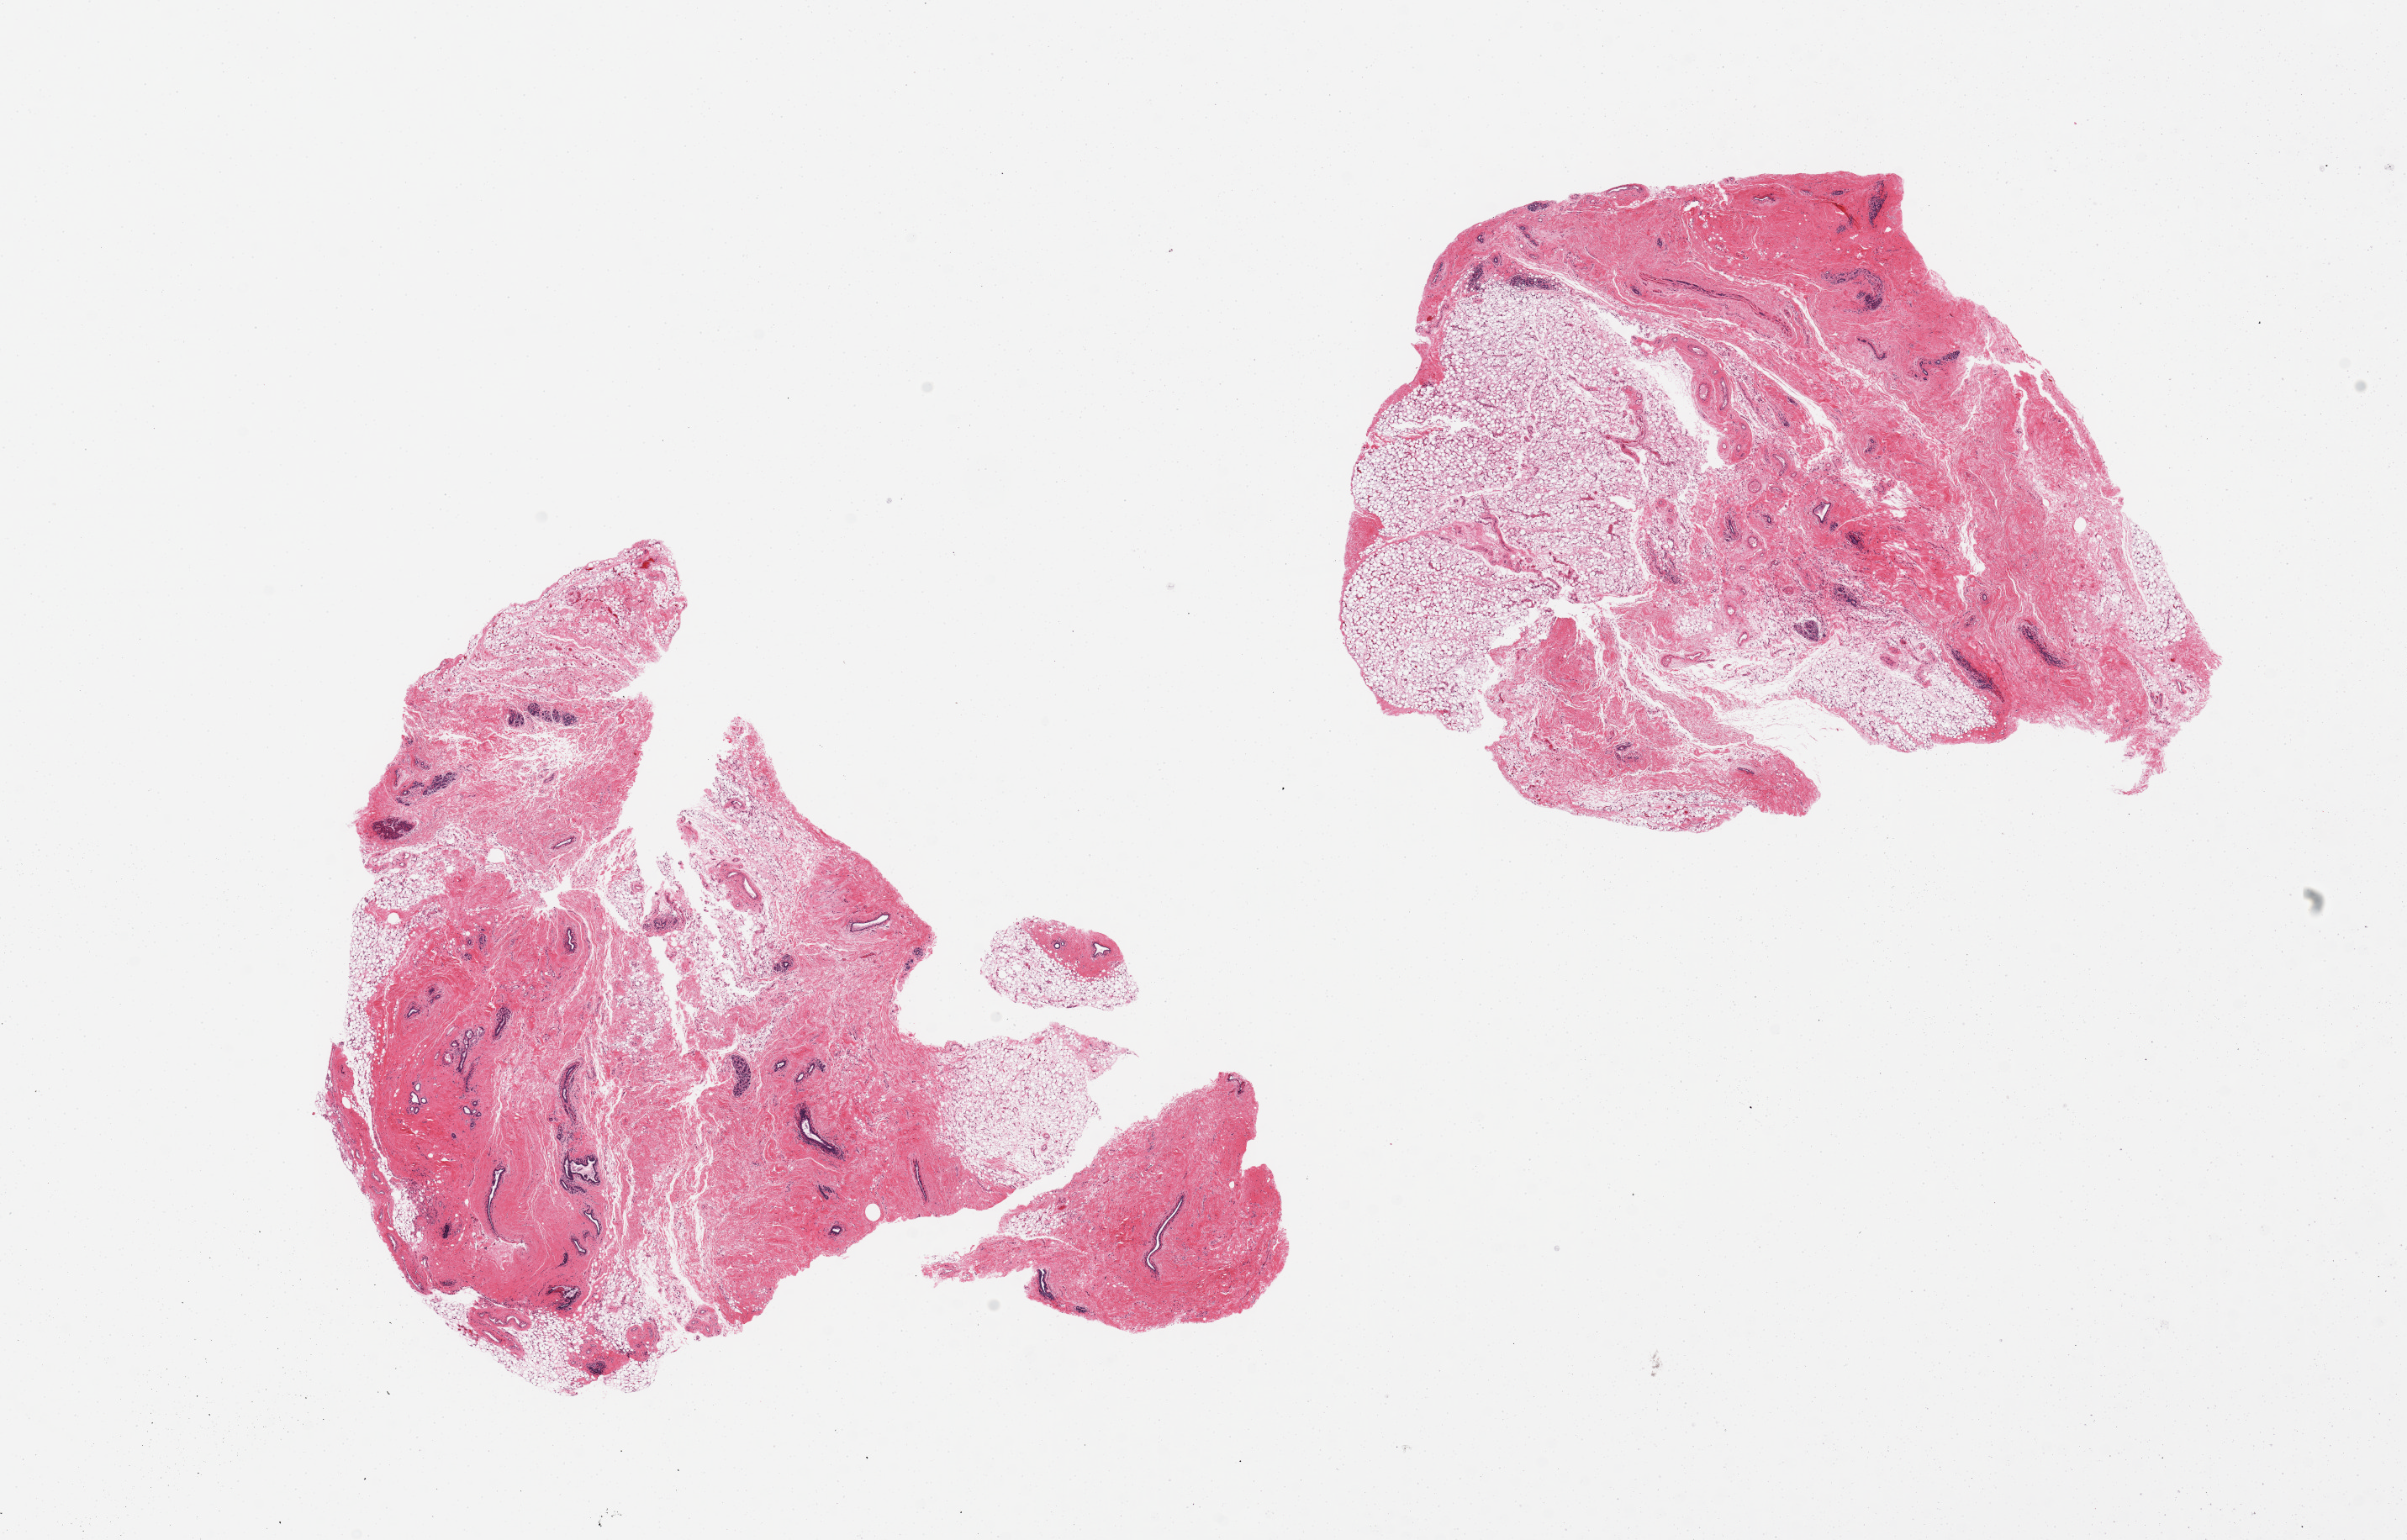
Whole-slide image, H&E stain, whole scanned area (about 22.6 x 14.5 mm) shown as a low-resolution overview, PAXgene-fixed paraffin-embedded (PFPE) section, sampled site (target tissue): breast, donor tissue sample. Donor sex: female.
- reviewer comment on this tissue sample: 2 pieces, fibrocystic changes, rep ductal/lobular elements